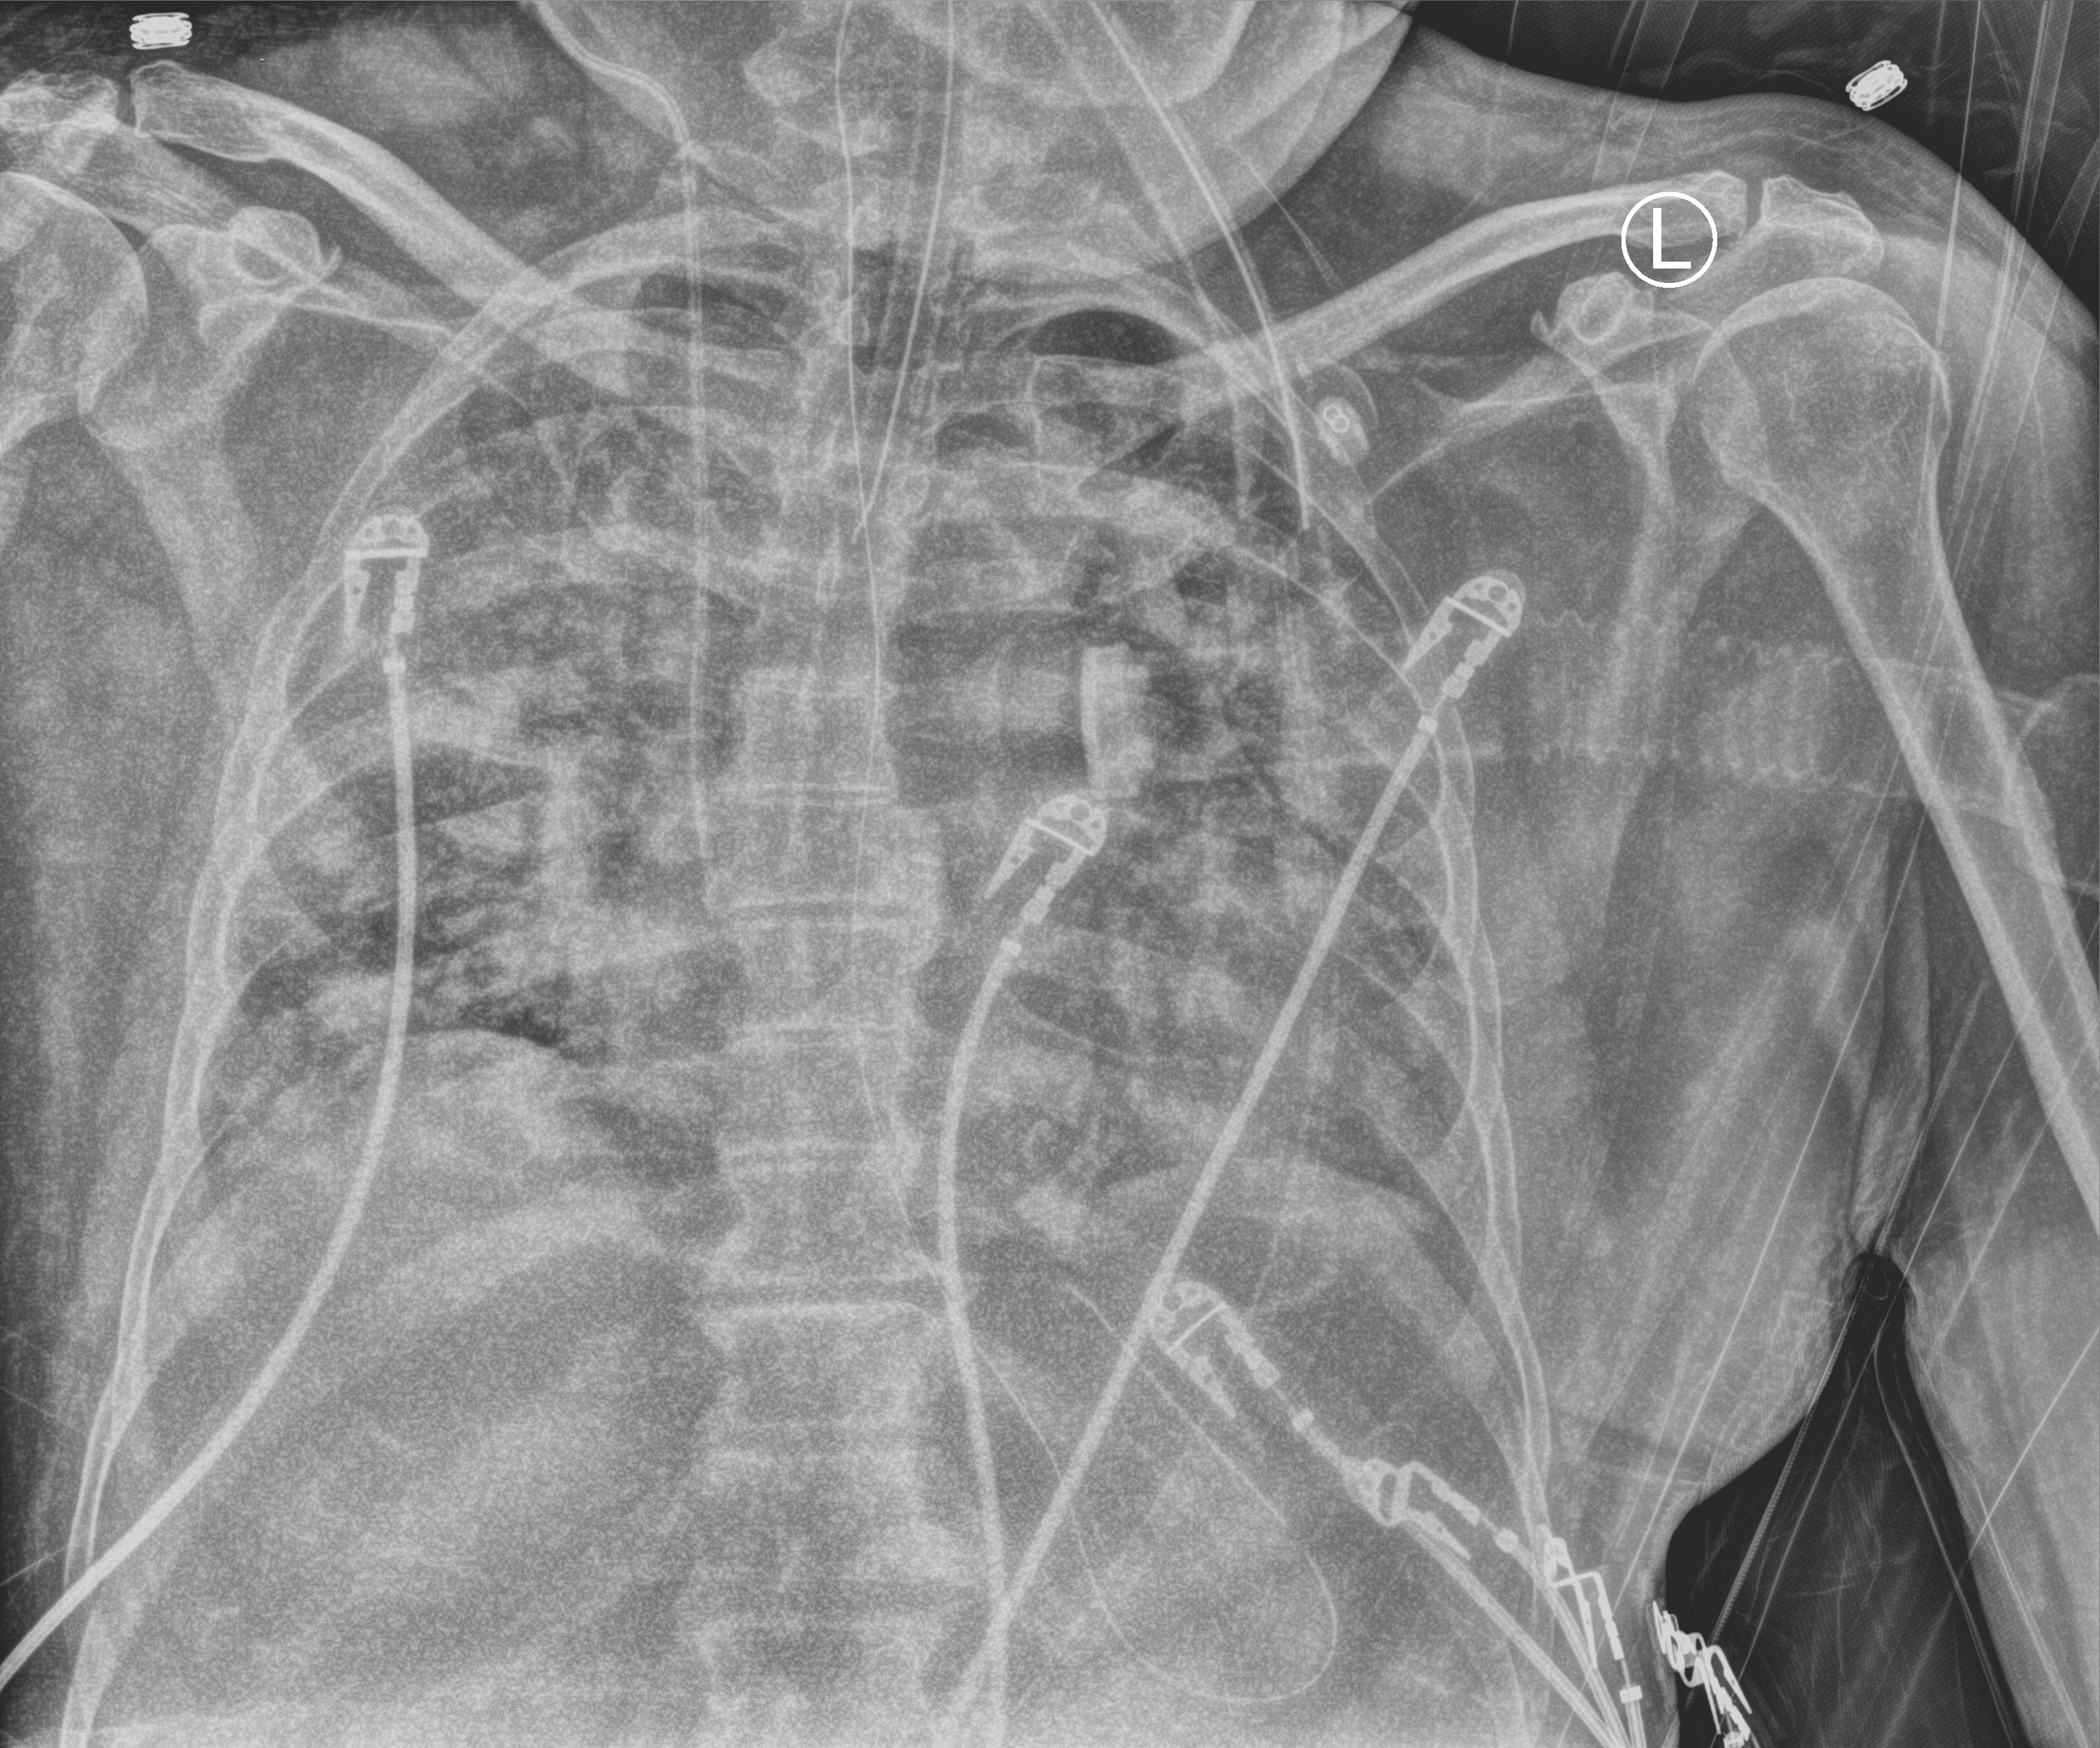
Bedside chest radiograph (computed radiography); anteroposterior (AP) projection. Male patient hospitalised with COVID-19, age 60–74 years.
From the hospital-stay record, not from the radiograph (when in the stay this image was taken is not recorded): mechanically ventilated during this hospital stay: yes; COPD (admission record): no; admitted to intensive care during this hospital stay: yes.